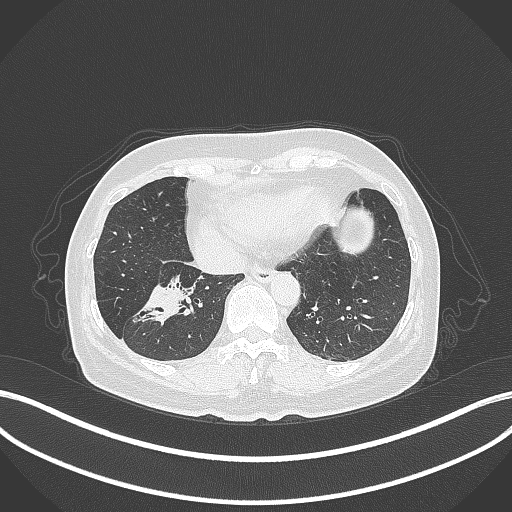
Chest CT, one axial slice; slice 115 of 429 in the series (ordered by position); 120 kVp; lung window (W 1500 / L -600 HU); 1 mm slice thickness; 512 × 512 image matrix, field of view 400 × 400 mm. Patient: female, 67 years. Case-level facts recorded for this patient, not image findings: clinical TNM (as recorded): T1c N1 M0; histopathological grade: G2-3.
Annotated regions visible in this slice (bounding box drawn by a radiologist):
- lung tumour (recorded histology: adenocarcinoma): bounding box [x1, y1, x2, y2] px = [133, 283, 195, 332]